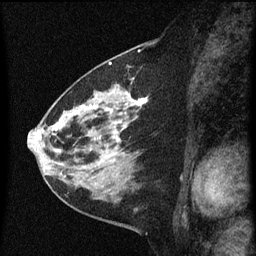
Breast MRI (dynamic contrast-enhanced), one sagittal slice. Dynamic contrast-enhanced series, image 2 of 3 at this slice position (ordered by acquisition). 1.5 T. TE 4.2 ms, TR 8 ms. 2 mm slice thickness. 256 × 256 image matrix, field of view 180 × 180 mm. Female patient, age 60 years.
Structures marked on this image (semi-automatic segmentation, software-assisted and operator-edited):
- analysis volume of interest (the breast-tissue region the enhancement analysis was run in; not a lesion): bounding box (x1, y1, x2, y2) in pixels: (48, 82, 149, 183)
- tumour enhancement mask (voxels above the 70 % enhancement threshold inside the analysis volume of interest): (53, 98, 148, 161)